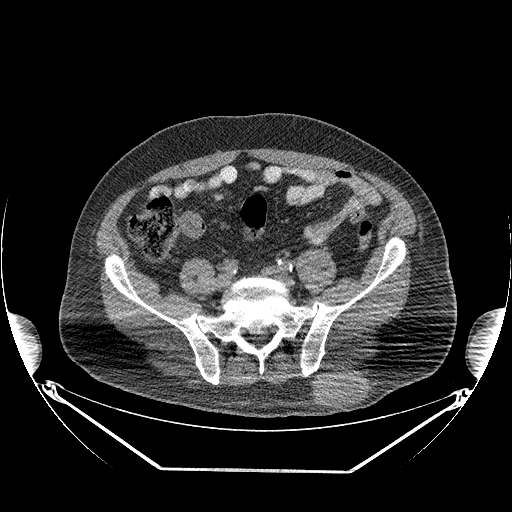
CT of an extremity soft-tissue mass (from a PET/CT study), one axial slice; slice 91 of 267 in the series (ordered by position); reconstruction kernel STANDARD; soft-tissue window (W 400 / L 40 HU); 3.75 mm slice thickness; 512 × 512 image matrix. Male patient. From the clinical record (not read from this slice): histological type: pleiomorphic leiomyosarcoma; grade: high; site of the primary tumour: left buttock.
Structures marked on this image (expert contour drawn on MRI and transferred to this co-registered scan by the dataset authors):
- gross tumour volume including surrounding oedema: bounding box (x1, y1, x2, y2) in pixels: (313, 368, 368, 408)
- gross tumour volume (mass): (313, 370, 366, 408)